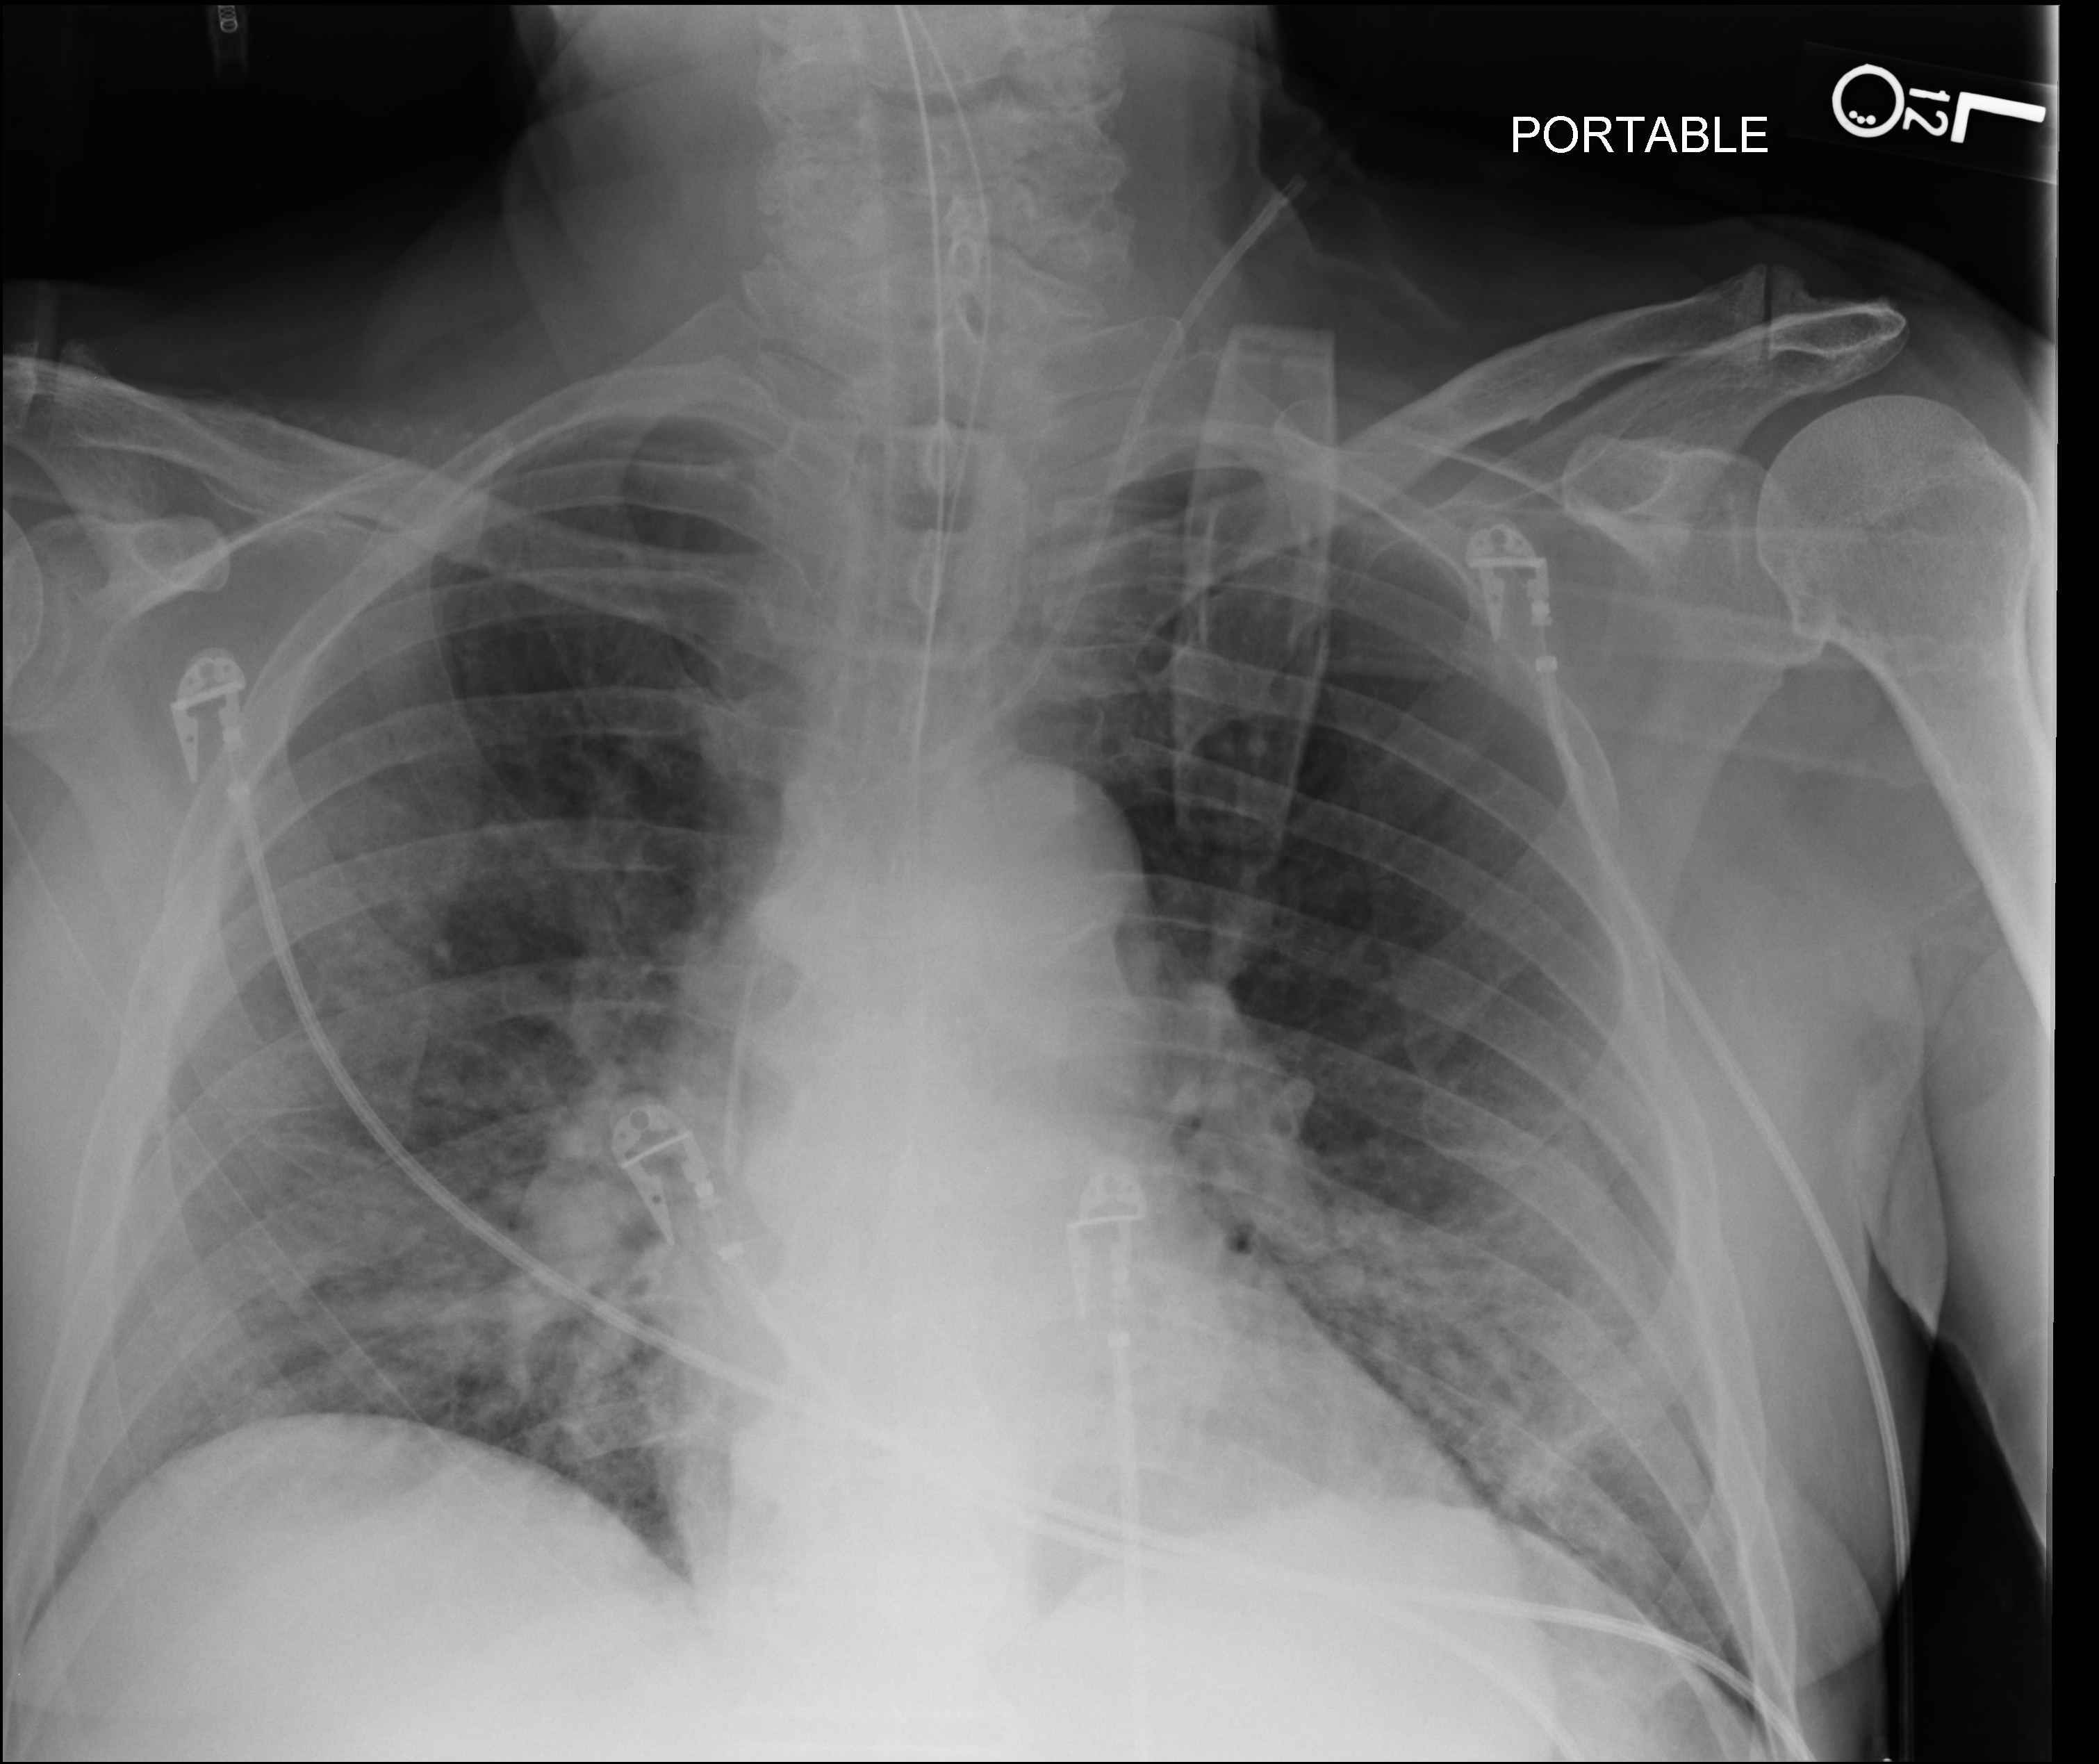
Chest X-ray (portable), anteroposterior (AP) projection. Male patient hospitalised with COVID-19, age 60–74 years.
Hospital-stay facts (about this admission, not read from this image; timing relative to this image not recorded):
- mechanically ventilated during this hospital stay: yes
- hypertension (admission record): yes